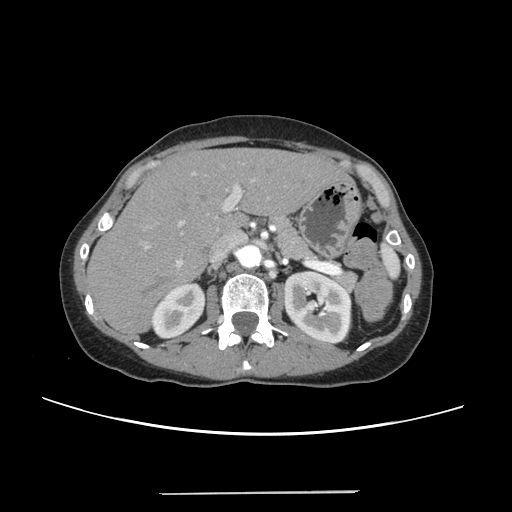
Contrast-enhanced abdominal CT, one axial slice; slice 154 of 240 in the series (ordered by position); 120 kVp; intravenous contrast given; soft-tissue window (W 400 / L 40 HU); 1.25 mm slice thickness; 512 × 512 image matrix, field of view 371 × 371 mm. Female patient, age 60 years. From the clinical record (not read from this slice): diagnosis: colorectal cancer liver metastases, imaged before liver resection; multiple liver metastases: no; largest metastasis: 1.5 cm; disease in both lobes: no.
Structures marked on this image (expert manual segmentation):
- liver: box from (x=89, y=149) to (x=346, y=332) px
- planned liver remnant (the part of the liver to remain after resection): (x=89, y=149)–(x=344, y=332)
- portal vein (with intrahepatic branches): (x=141, y=171)–(x=257, y=267)